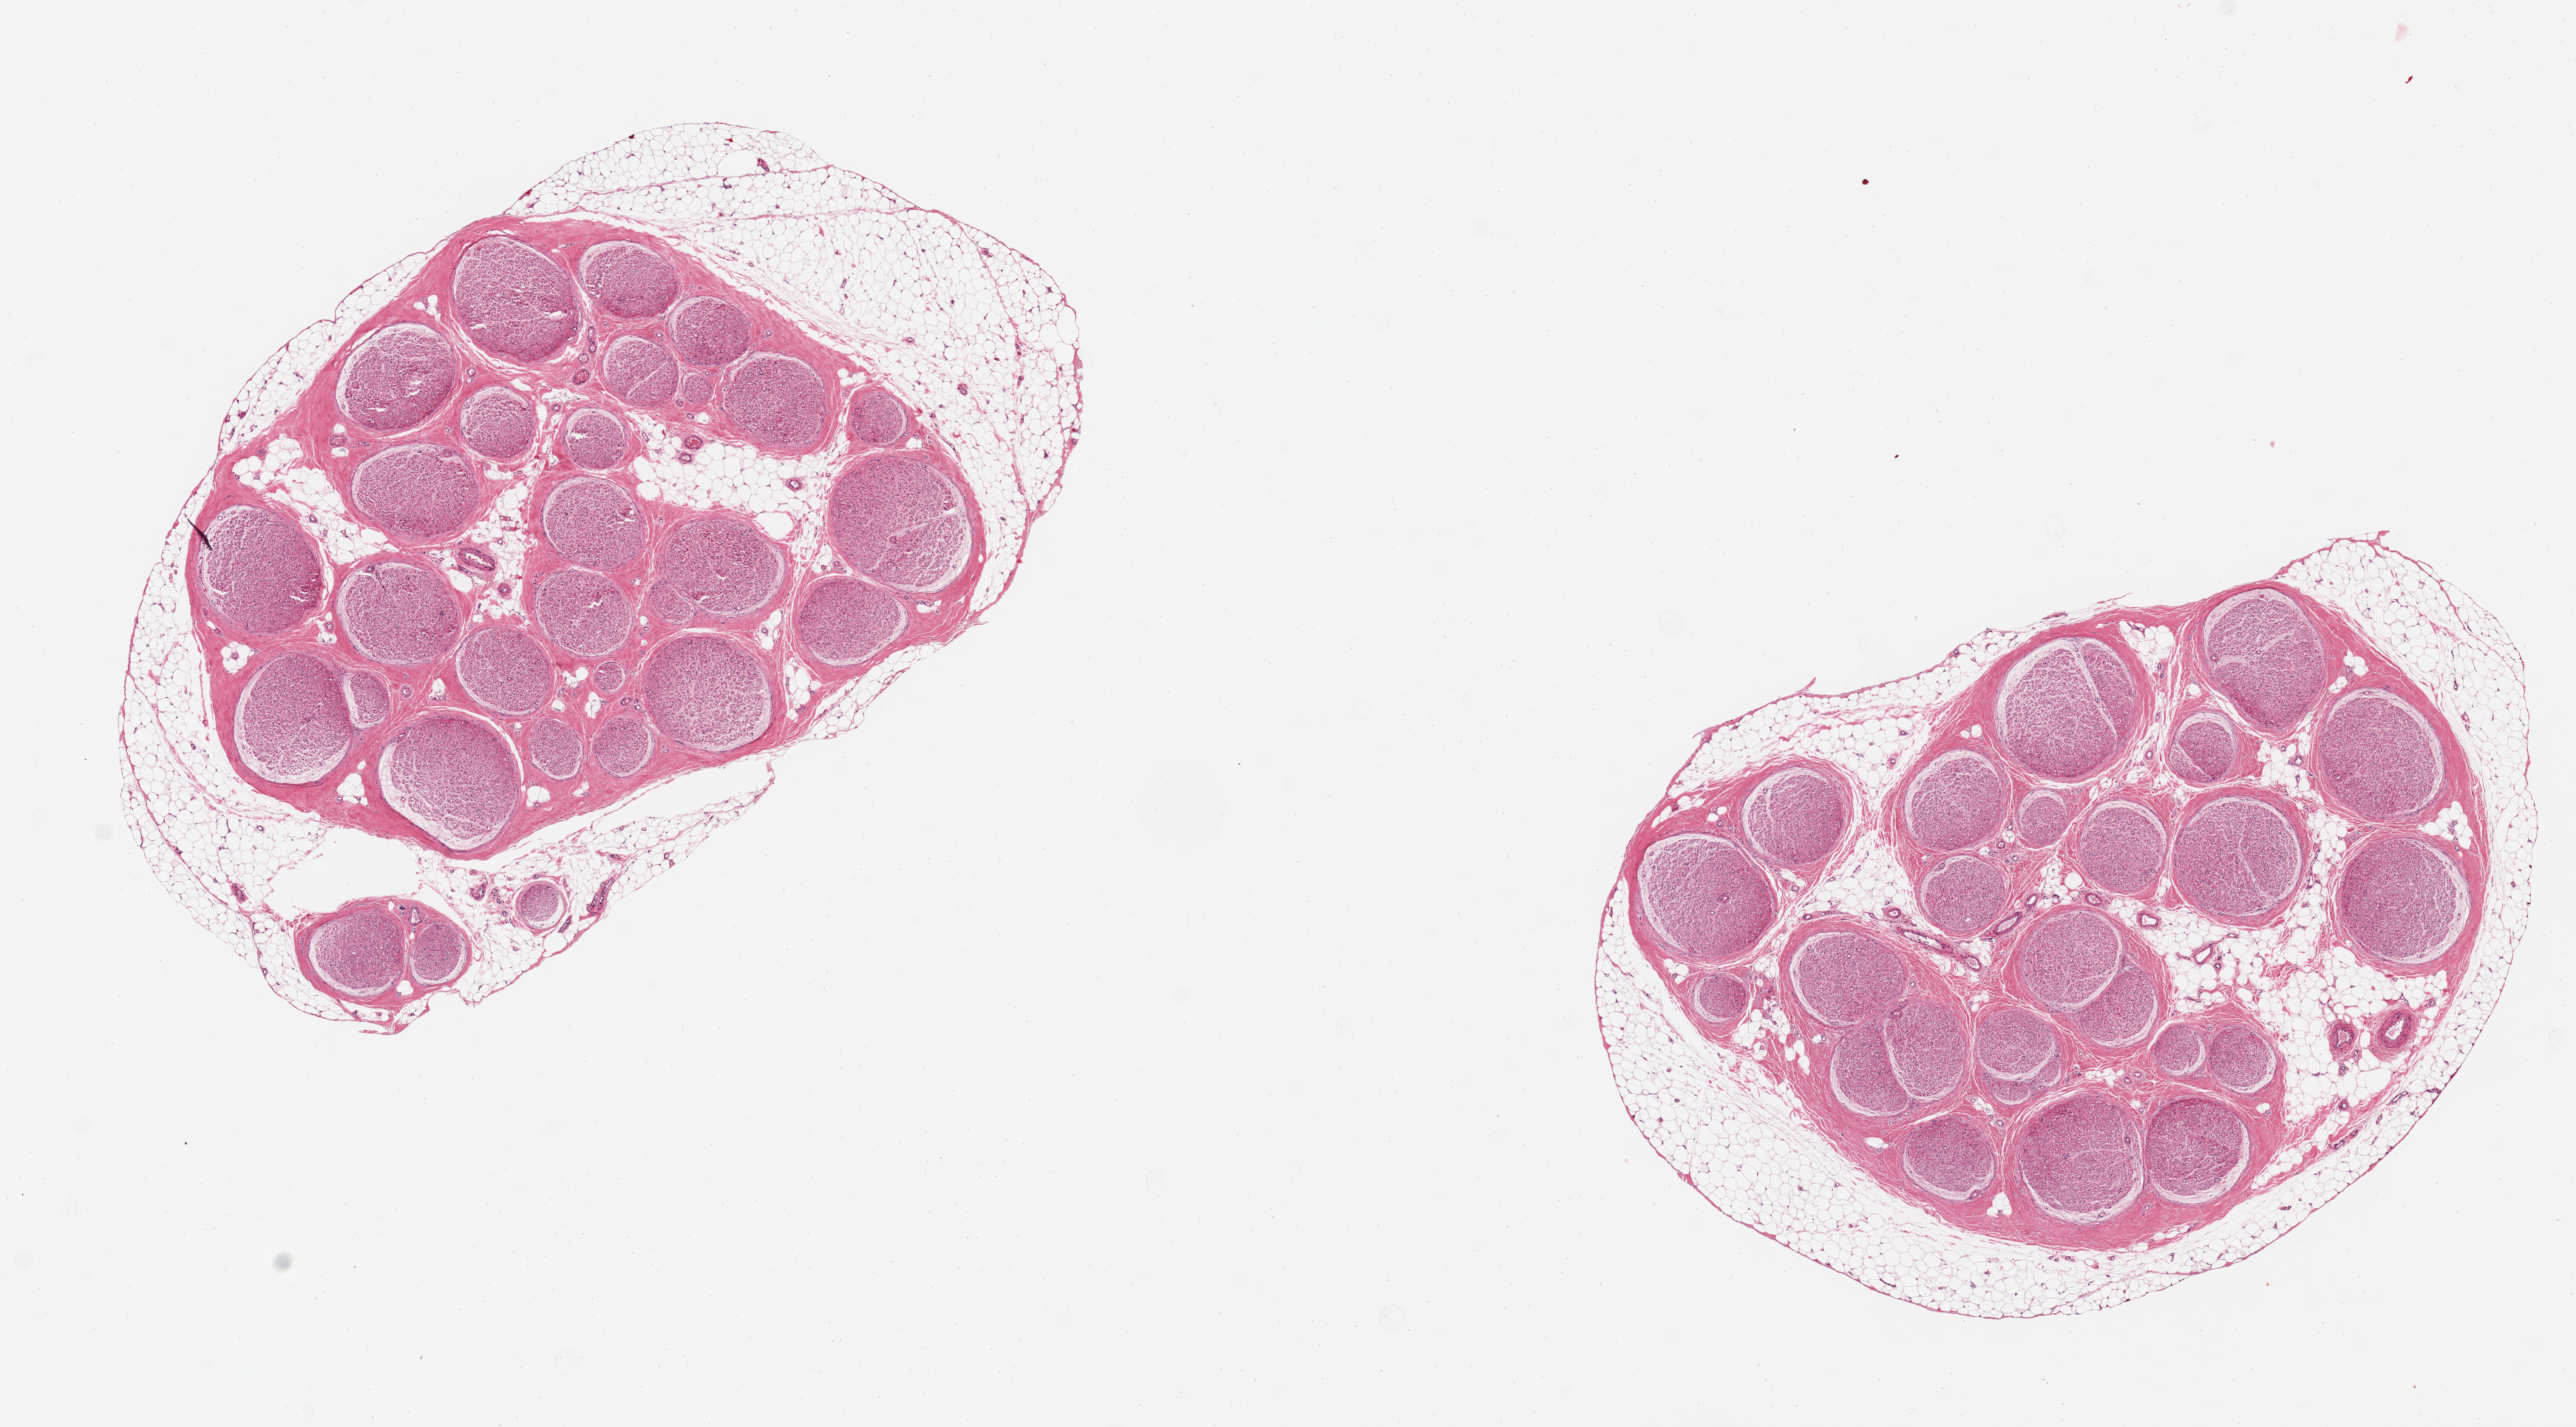
H&E whole-slide image, brightfield, whole scanned area (about 13.8 x 7.6 mm) shown as a low-resolution overview. PAXgene-fixed paraffin-embedded (PFPE) section. Target tissue: tibial nerve. Tissue donor sample. Donor sex: female.
• reviewer comment on this tissue sample: 2 pieces, 5x3 & 5x4 mm; ~30% adipose in and around nerve bundles